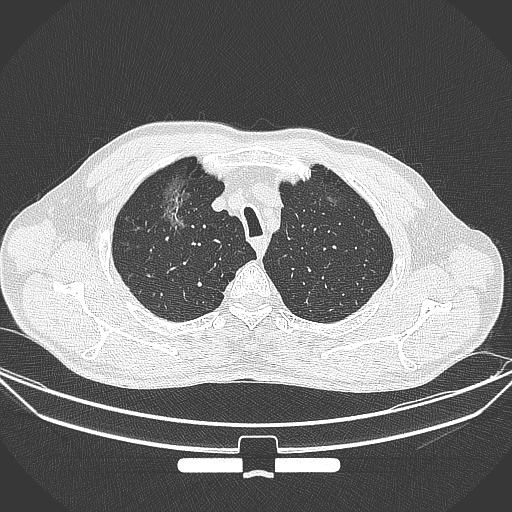
Chest CT, one axial slice. Slice 289 of 355 in the series (ordered by position). Lung window (W 1500 / L -600 HU). 1 mm slice thickness. 512 × 512 image matrix, field of view 399 × 399 mm. Male patient, age 67 years. Case-level facts recorded for this patient, not image findings: clinical TNM (as recorded): T1c N0 M0; histopathological grade: G2.
Outlined on this slice (bounding box drawn by a radiologist):
- lung tumour (recorded histology: adenocarcinoma): box from (x=153, y=168) to (x=189, y=230) px